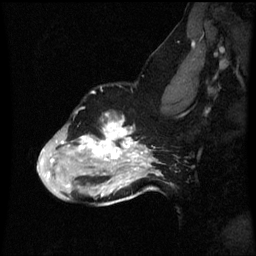
Breast MRI (dynamic contrast-enhanced), one sagittal slice. Position 42 of 60 along the scan axis. Dynamic contrast-enhanced series, image 2 of 3 at this slice position (ordered by acquisition). 1.5 T. TE 4.2 ms, TR 8.9 ms. 256 × 256 image matrix, field of view 200 × 200 mm. Patient: female, 49 years. Case-level facts recorded for this patient, not image findings: setting: breast cancer imaged before/during neoadjuvant chemotherapy; receptor status: HR-positive, HER2-negative.
Annotated regions visible in this slice (semi-automatic segmentation, software-assisted and operator-edited):
- analysis volume of interest (the breast-tissue region the enhancement analysis was run in; not a lesion): bounding box [x1, y1, x2, y2] px = [38, 112, 159, 199]
- tumour enhancement mask (voxels above the 70 % enhancement threshold inside the analysis volume of interest): [50, 120, 159, 177]